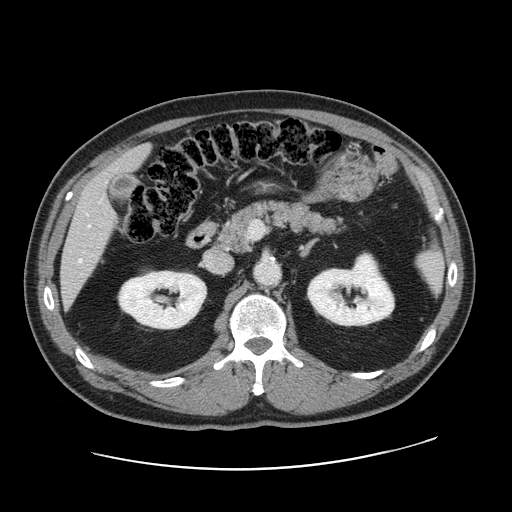
Contrast-enhanced abdominal CT, one axial slice. Slice 82 of 178 in the series (ordered by position). 120 kVp. Intravenous contrast given. Soft-tissue window (W 400 / L 40 HU). 2.5 mm slice thickness. 512 × 512 image matrix, field of view 403 × 403 mm. Male patient, age 63 years. From the clinical record (not read from this slice): diagnosis: colorectal cancer liver metastases, imaged before liver resection; multiple liver metastases: yes; largest metastasis: 8 cm; disease in both lobes: yes.
Annotated regions visible in this slice (outlined manually by an expert reader):
- hepatic veins: box from (x=79, y=225) to (x=90, y=261) px
- liver: (x=62, y=147)–(x=149, y=302)
- planned liver remnant (the part of the liver to remain after resection): (x=111, y=147)–(x=149, y=172)